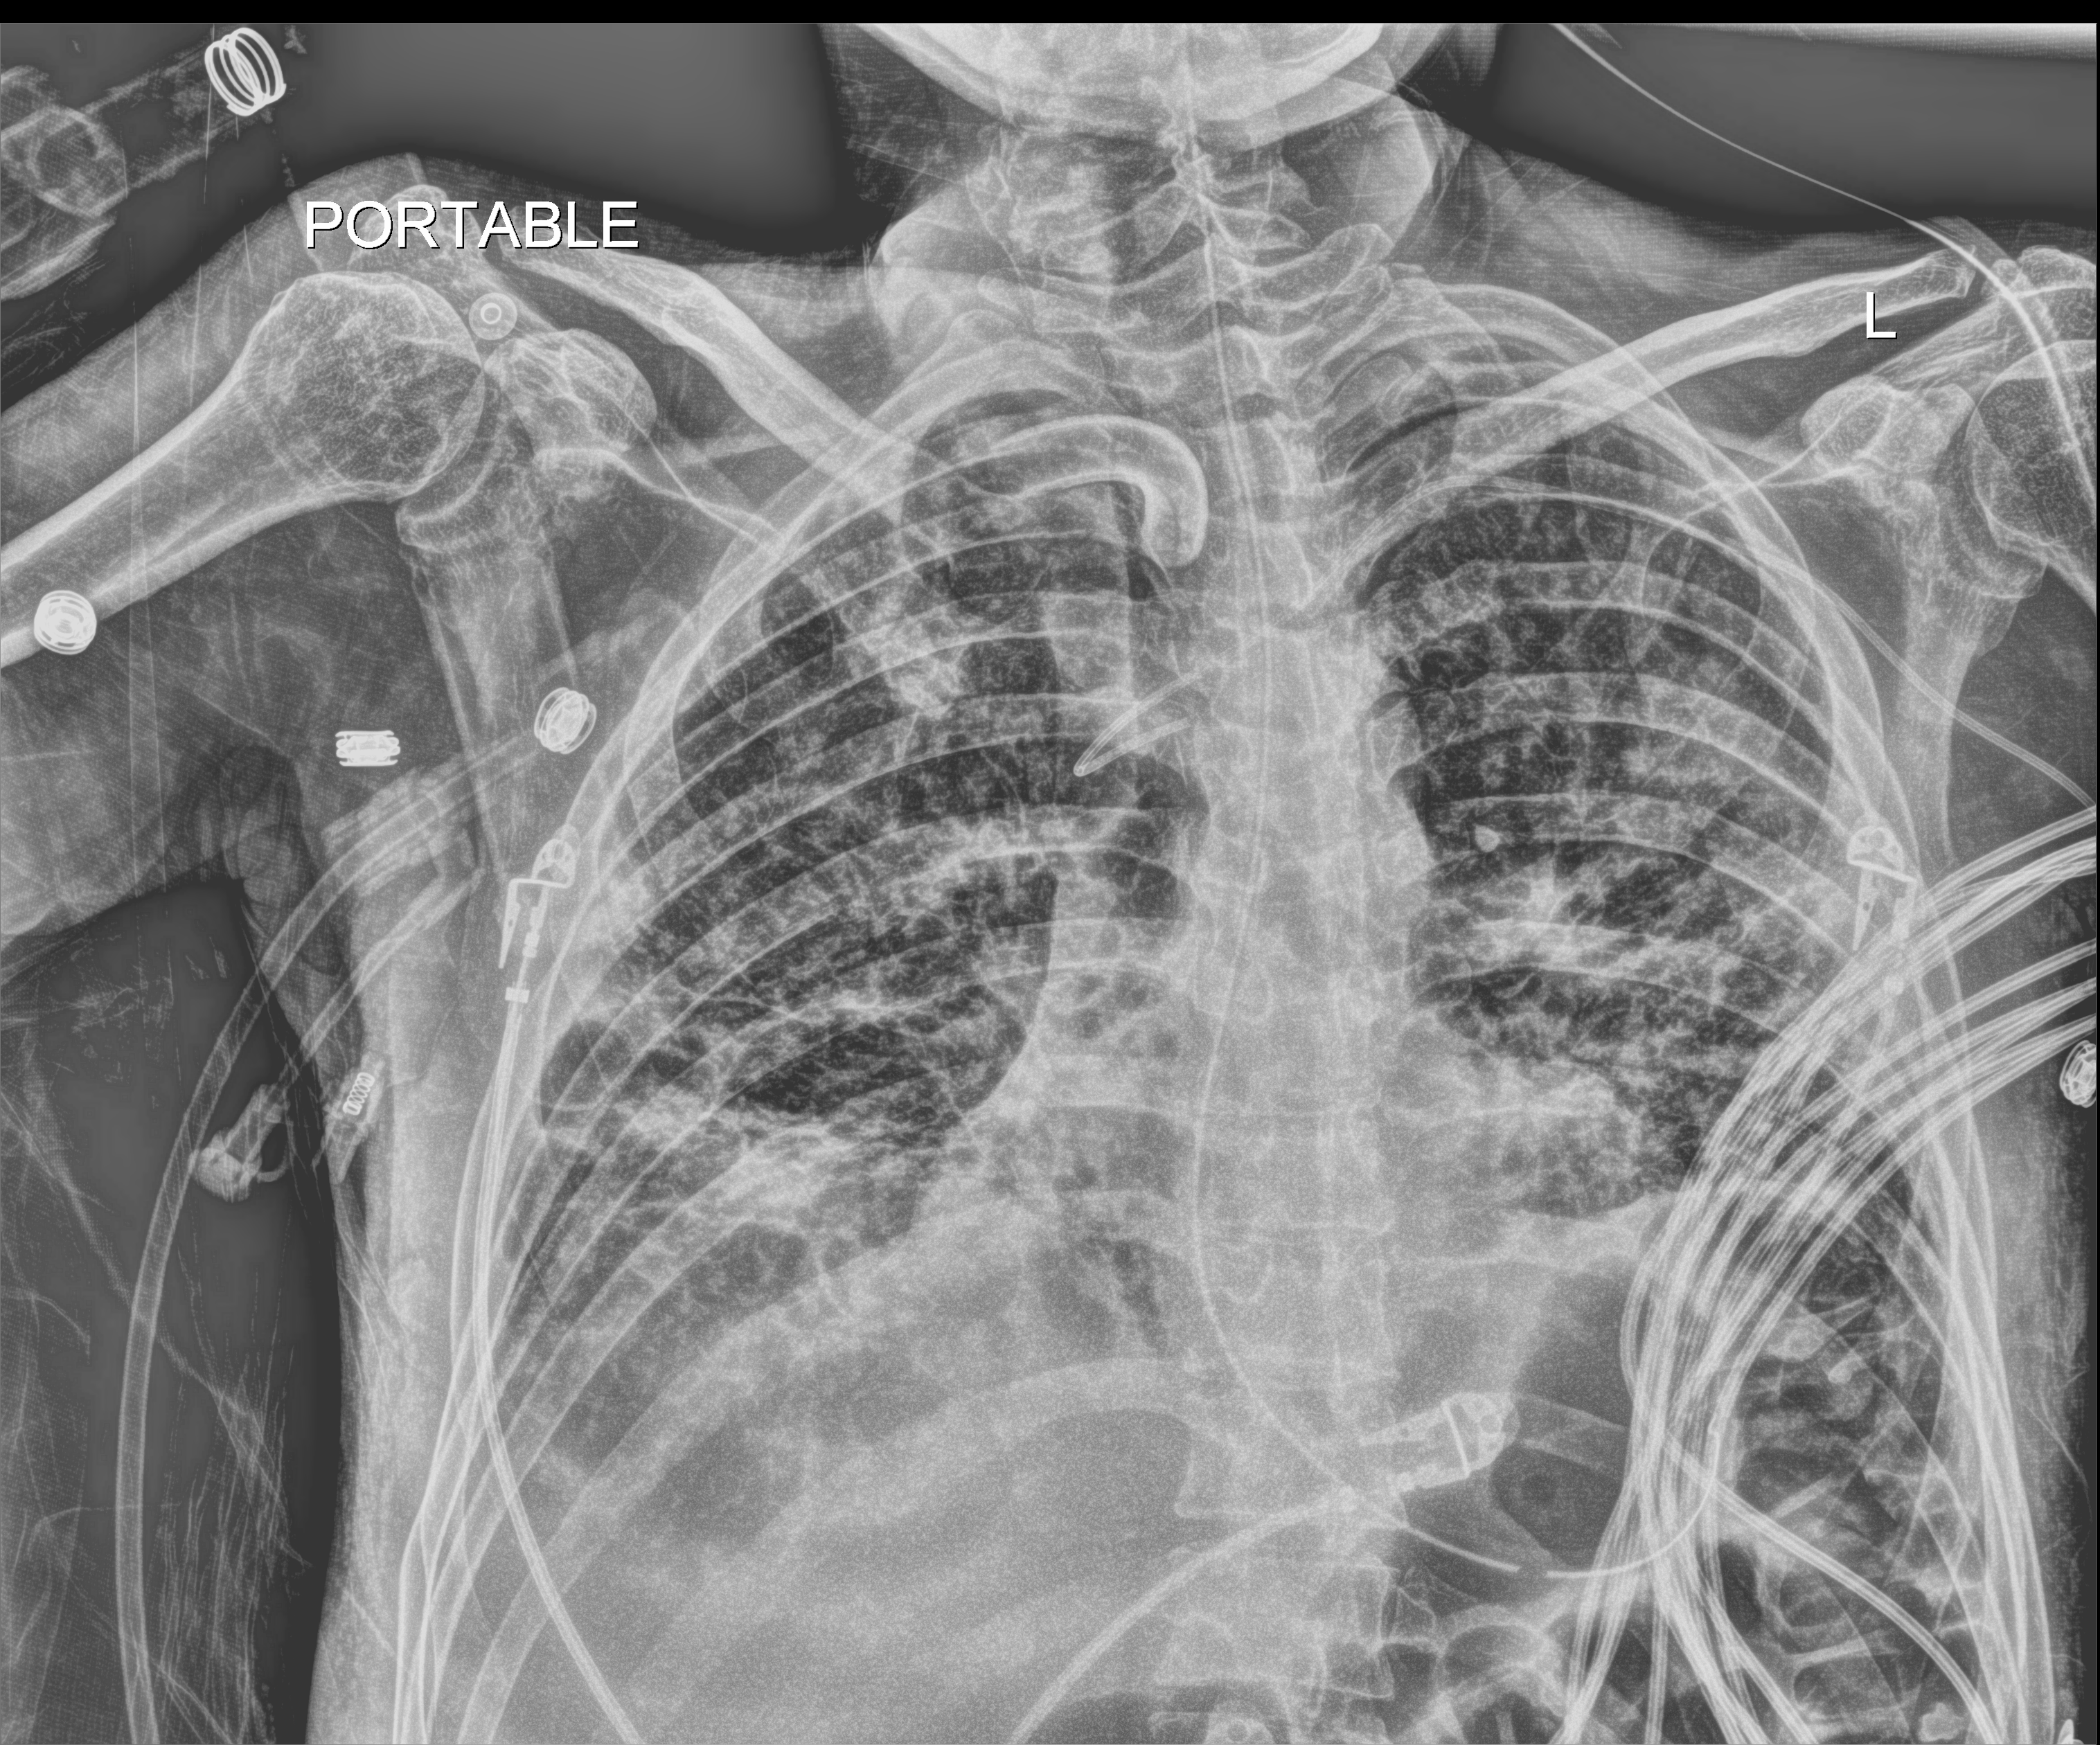
Bedside chest radiograph (digital radiography); anteroposterior (AP) projection. Patient hospitalised with COVID-19; male, aged 18–59 years.
From the hospital-stay record, not from the radiograph (when in the stay this image was taken is not recorded):
- length of hospital stay: 96 days
- mechanically ventilated during this hospital stay: yes
- admitted to intensive care during this hospital stay: yes